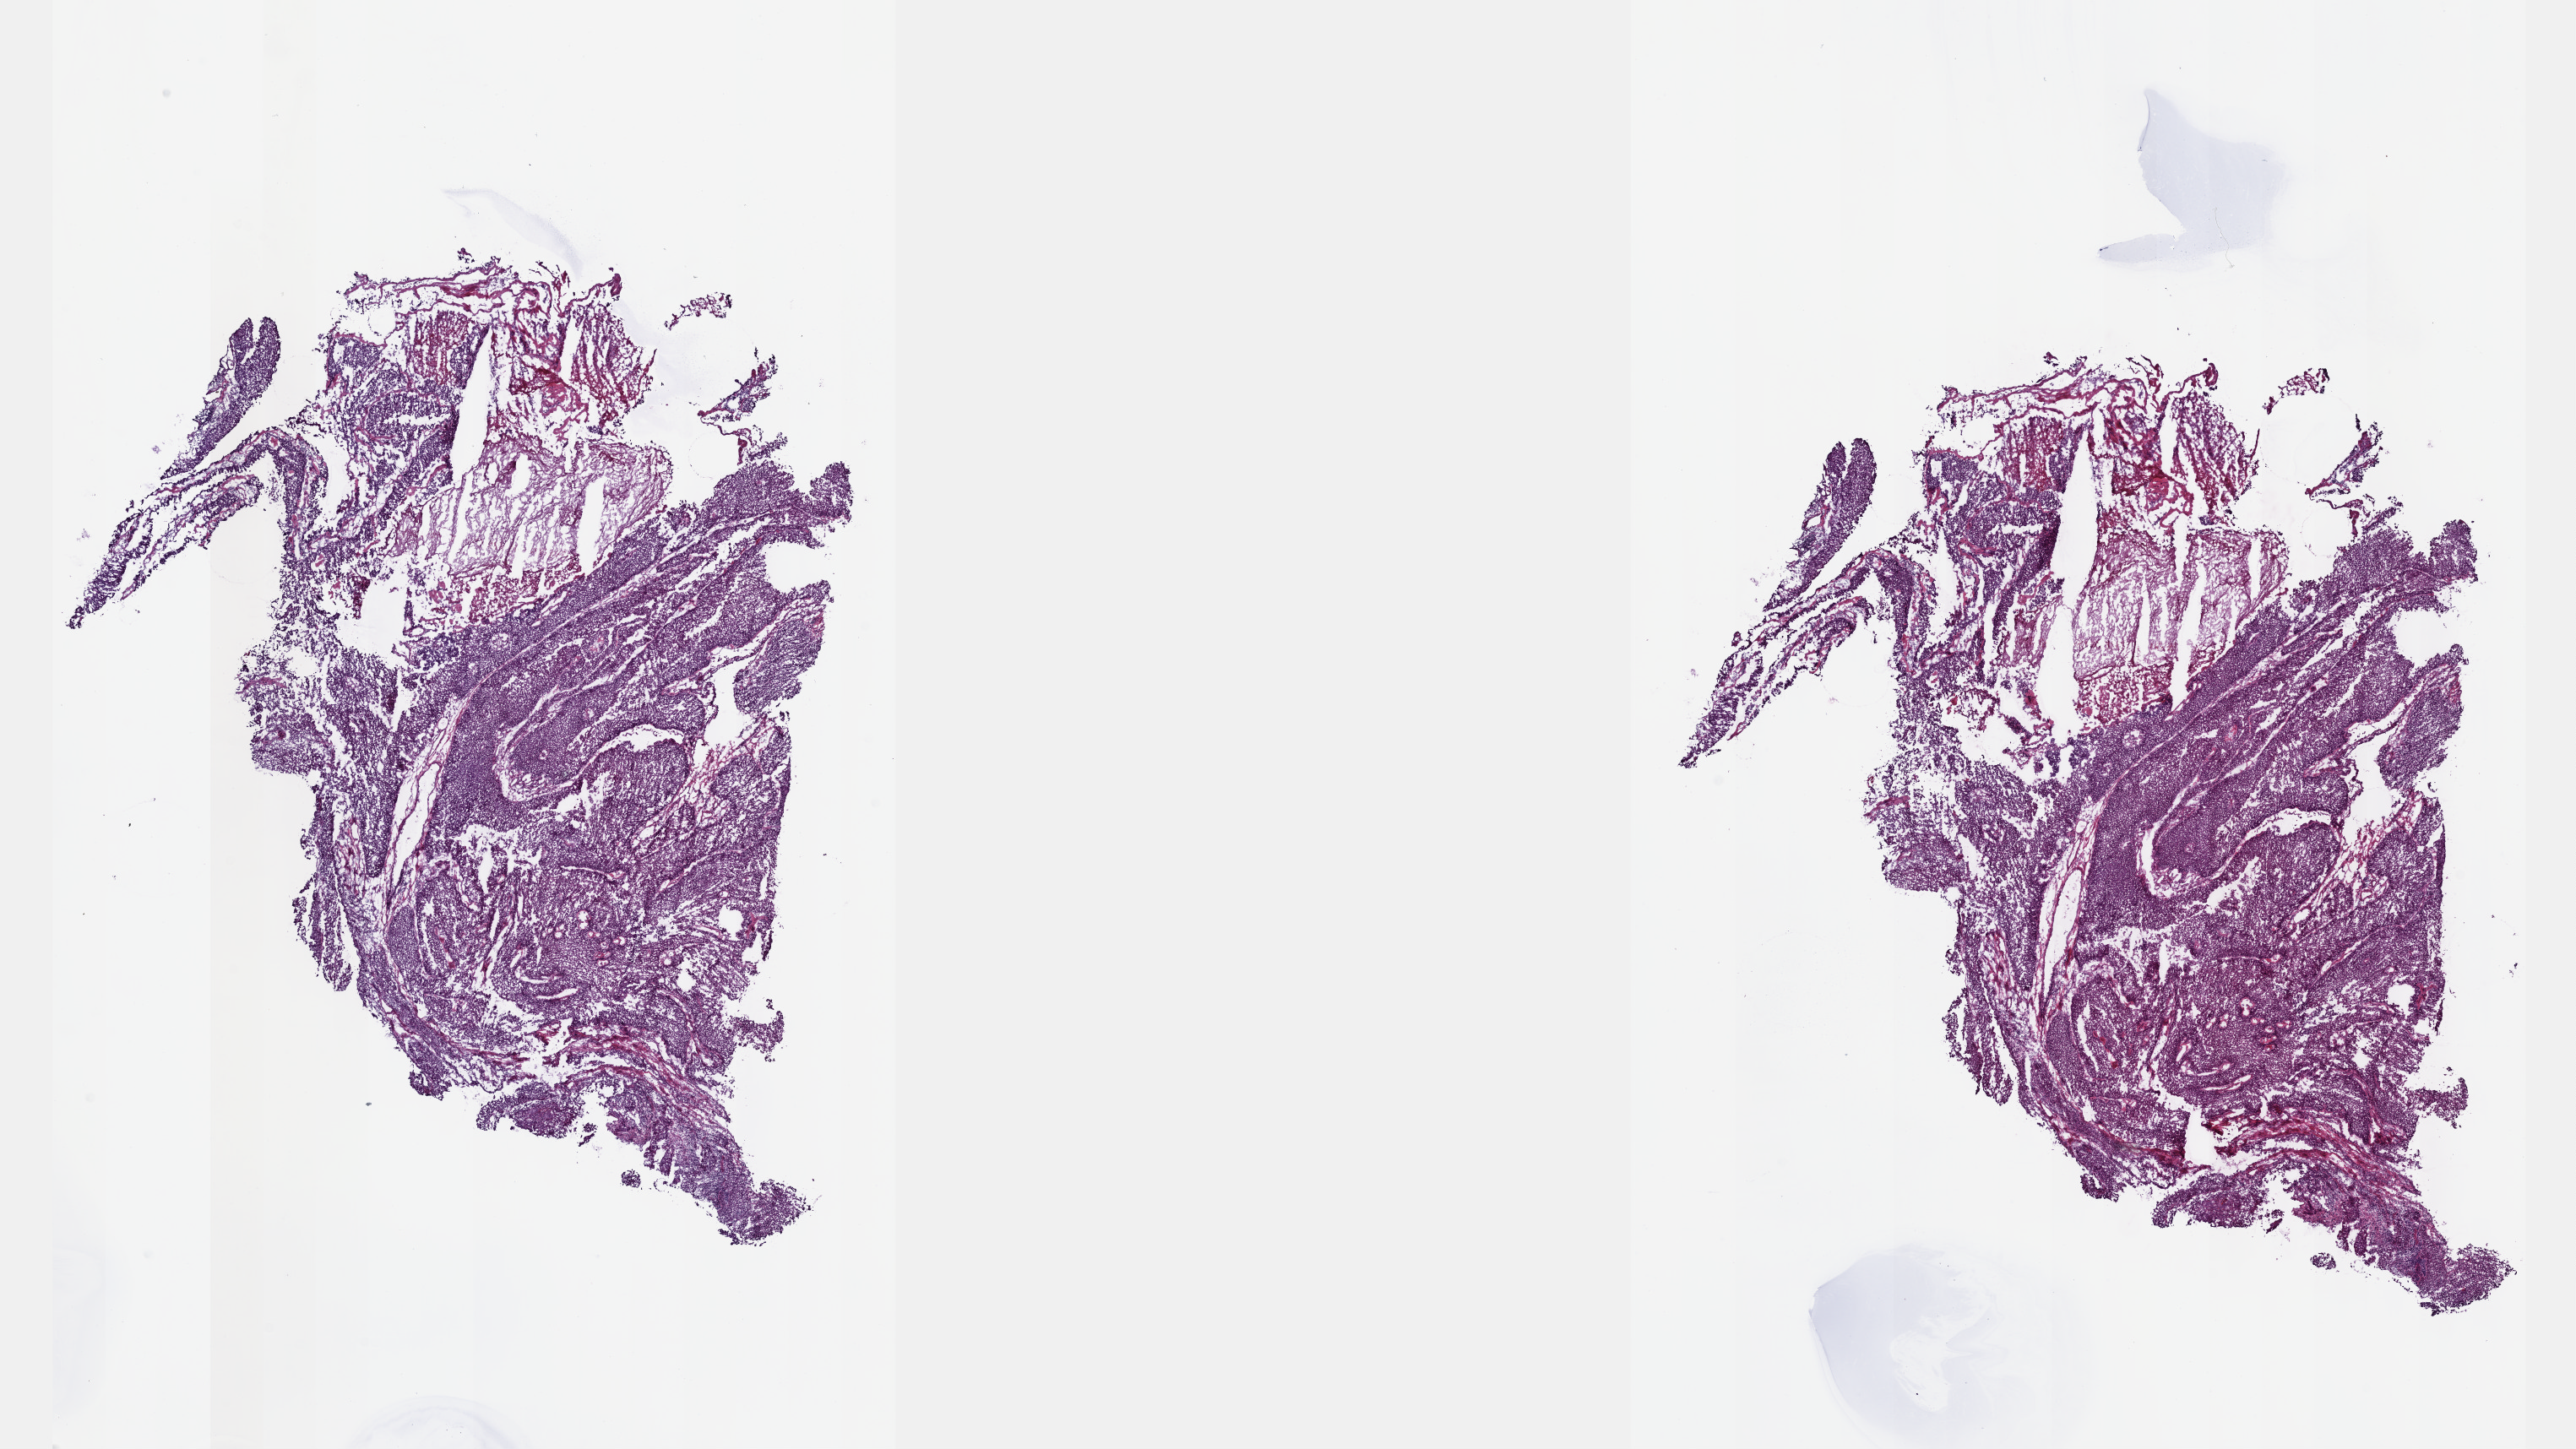
Digitized H&E tissue section (whole slide), a low-resolution overview of the entire scanned area, about 24.6 x 13.9 mm (from a 40x scan); frozen section from the top of the tissue portion; bladder, primary tumour sample. Male patient; age at initial diagnosis 60 years. Histologic grade: high grade. Composition of this section per pathologist review: tumour cells 73%, tumour nuclei 87%, normal cells 0%, stromal cells 10%, necrosis 17%. Infiltration values recorded for this section: lymphocyte infiltration 10%, monocyte infiltration 0%, neutrophil infiltration 0%.
Lymph nodes positive (case pathology): 0 of 10 examined. Pathologic diagnosis: Papillary transitional cell carcinoma (trigone of bladder). AJCC pathologic stage: IV (7th edition).